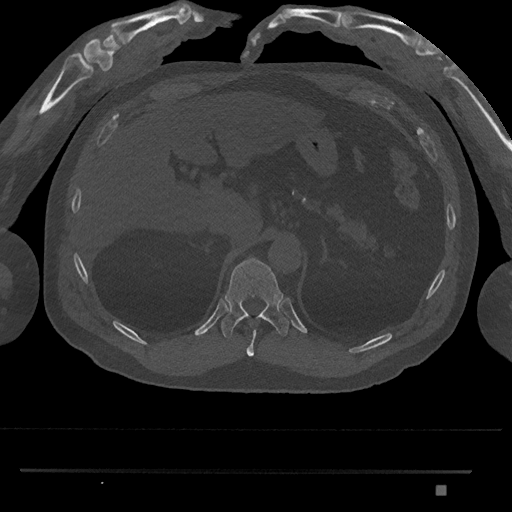
CT including the spine, one axial slice. Slice 959 of 1134 in the series (ordered by position). Reconstruction kernel Br40s/3. Bone window (W 1800 / L 400 HU). 0.5 mm slice thickness. 512 × 512 image matrix, field of view 429 × 429 mm. Patient: male, 65 years. Case-level facts recorded for this patient, not image findings: primary cancer: prostate.
Structures marked on this image (semi-automatic segmentation, software-assisted and operator-edited):
- T10 vertebra: bounding box [x1, y1, x2, y2] px = [246, 330, 256, 357]
- T11 vertebra: [221, 258, 289, 338]